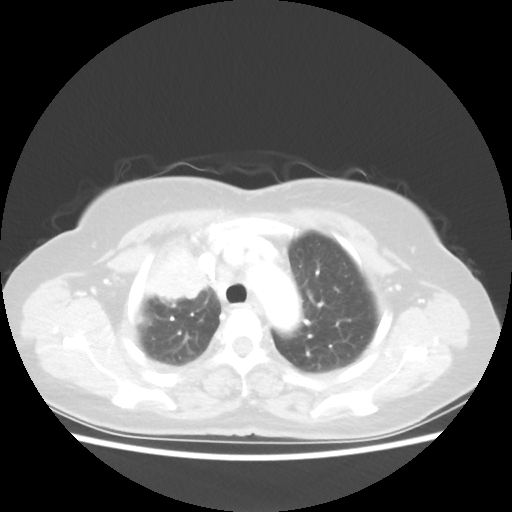
Chest CT, one axial slice. Position 42 of 55 along the scan axis. Reconstruction kernel STANDARD. Lung window (W 1500 / L -600 HU). 5 mm slice thickness. 512 × 512 image matrix. Patient: female, 62 years. From the clinical record (not read from this slice): clinical TNM (as recorded): T4 N3 M0.
Outlined on this slice (rectangle marked by the reading radiologist):
- lung tumour (recorded histology: squamous cell carcinoma): bounding box (x1, y1, x2, y2) in pixels: (131, 233, 220, 309)